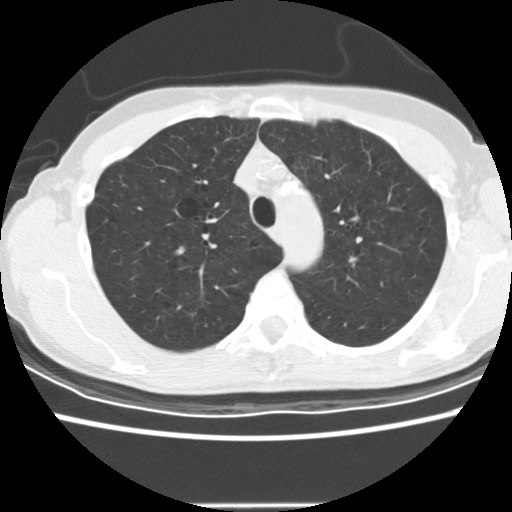
Axial slice from a low-dose chest CT screening exam, second annual screen, lung window (W 1500 / L -600 HU), 2.5 mm slice thickness, standard (soft-tissue) reconstruction kernel (STANDARD), 120 kVp, slice 38 of 166 in the series. Female participant, aged 58 years at enrolment. Current smoker at enrolment.
Expert-annotated lung lesion, bounding box (x1, y1, x2, y2) in pixels: (174, 301, 208, 330). The screening reader recorded 2 non-calcified nodules or masses ≥4 mm on this exam; which of them this box marks is not recorded. Official screen result: positive, change unspecified: nodule(s) >= 4 mm or enlarging nodule(s), mass(es), or other non-specific abnormalities suspicious for lung cancer. Lung cancer was diagnosed 434 days after this screen (after the third annual screen): bronchiolo-alveolar adenocarcinoma, NOS, right upper lobe, well differentiated (G1), stage IA (AJCC 6th edition), 8 mm at pathology.